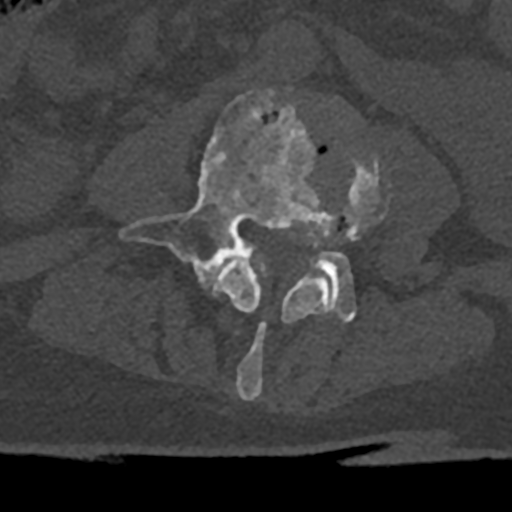
CT including the spine, one axial slice. Position 283 of 797 along the scan axis. Reconstruction kernel Br40s/3. 120 kVp. Bone window (W 1800 / L 400 HU). 0.5 mm slice thickness. 512 × 512 image matrix, field of view 160 × 160 mm. Male patient, age 74 years. From the clinical record (not read from this slice): primary cancer: renal.
Annotated regions visible in this slice (semi-automatic segmentation, software-assisted and operator-edited):
- L3 vertebra: bounding box <214,158,384,399> (left, top, right, bottom; pixels)
- L4 vertebra: <120,89,356,323>